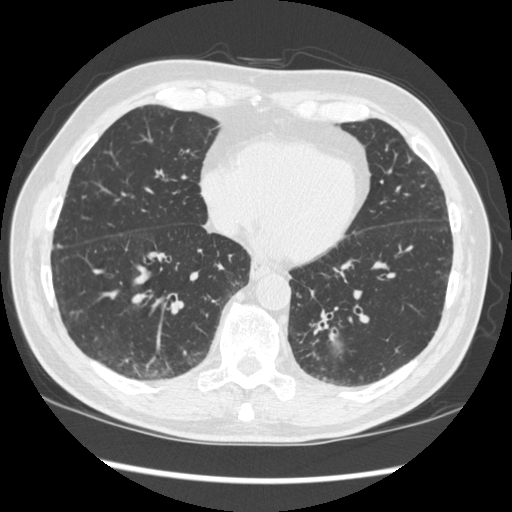
Axial slice from a low-dose chest CT screening exam. First (baseline) screen. Lung window (W 1500 / L -600 HU). Standard (soft-tissue) reconstruction kernel (STANDARD). Male, age 72 years at enrolment.
Expert reader's lesion annotation, box from (x=274, y=294) to (x=379, y=383) px. The screening reader recorded 2 non-calcified nodules or masses ≥4 mm on this exam (left lower lobe, right middle lobe); which of them this box marks is not recorded.